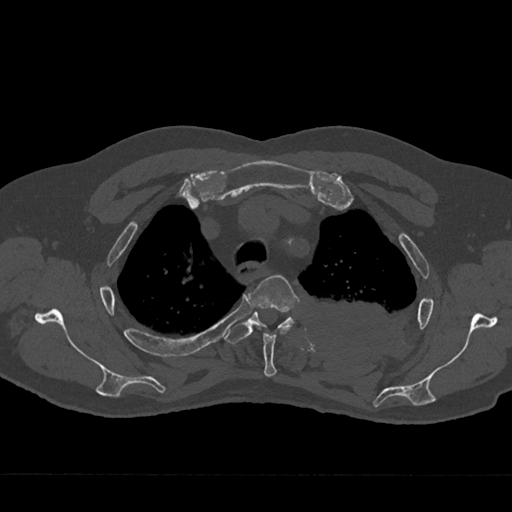
CT including the spine, one axial slice; position 546 of 797 along the scan axis; 120 kVp; bone window (W 1800 / L 400 HU); 512 × 512 image matrix. Patient: male, 75 years. From the clinical record (not read from this slice): primary cancer: renal; vertebrae with lytic lesions (as recorded): T4.
Annotated regions visible in this slice (semi-automatically segmented with operator editing):
- T3 vertebra: bounding box <249,275,300,377> (left, top, right, bottom; pixels)
- T4 vertebra: <224,312,295,344>